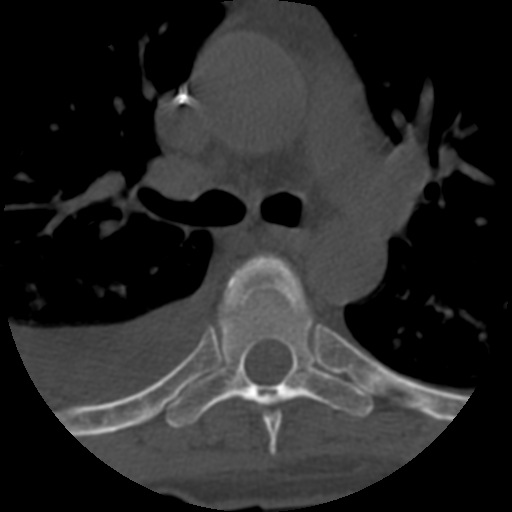
CT including the spine, one axial slice; position 441 of 708 along the scan axis; 120 kVp; one of 3 acquisitions stored at this slice position; bone window (W 1800 / L 400 HU); 1.25 mm slice thickness; 512 × 512 image matrix, field of view 160 × 160 mm. Patient age 55 years. From the clinical record (not read from this slice): primary cancer: colon; vertebrae with lytic lesions (as recorded): T12, L1, L5.
Annotated regions visible in this slice (semi-automatically segmented with operator editing):
- T5 vertebra: bounding box <264,413,281,456> (left, top, right, bottom; pixels)
- T6 vertebra: <166,253,373,429>